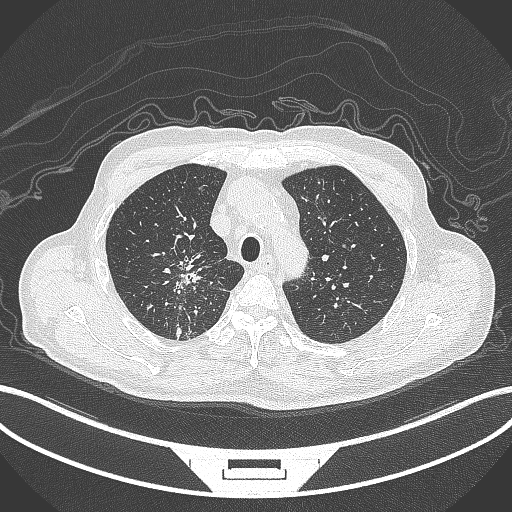
Chest CT, one axial slice; position 294 of 407 along the scan axis; lung window (W 1500 / L -600 HU); 512 × 512 image matrix, field of view 400 × 400 mm. Patient: male, 69 years. Case-level facts recorded for this patient, not image findings: clinical TNM (as recorded): T1c N1 M1.
Structures marked on this image (bounding box drawn by a radiologist):
- lung tumour (recorded histology: adenocarcinoma): bounding box <169,252,212,302> (left, top, right, bottom; pixels)